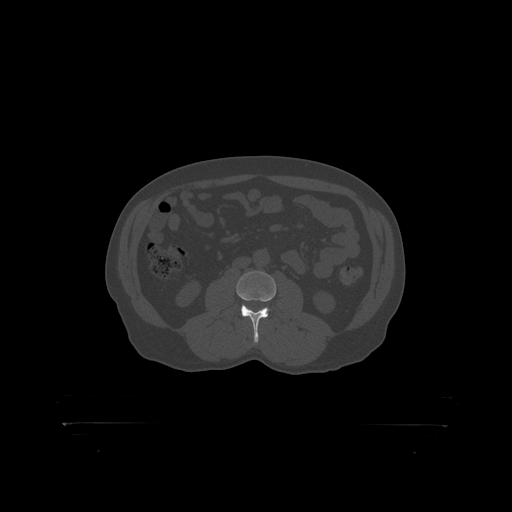
CT including the spine, one axial slice. Position 263 of 399 along the scan axis. Reconstruction kernel STANDARD. 120 kVp. Bone window (W 1800 / L 400 HU). 512 × 512 image matrix. Male patient, age 46 years. Case-level facts recorded for this patient, not image findings: primary cancer: skin.
Structures marked on this image (semi-automatically segmented with operator editing):
- L3 vertebra: box from (x=236, y=271) to (x=277, y=319) px